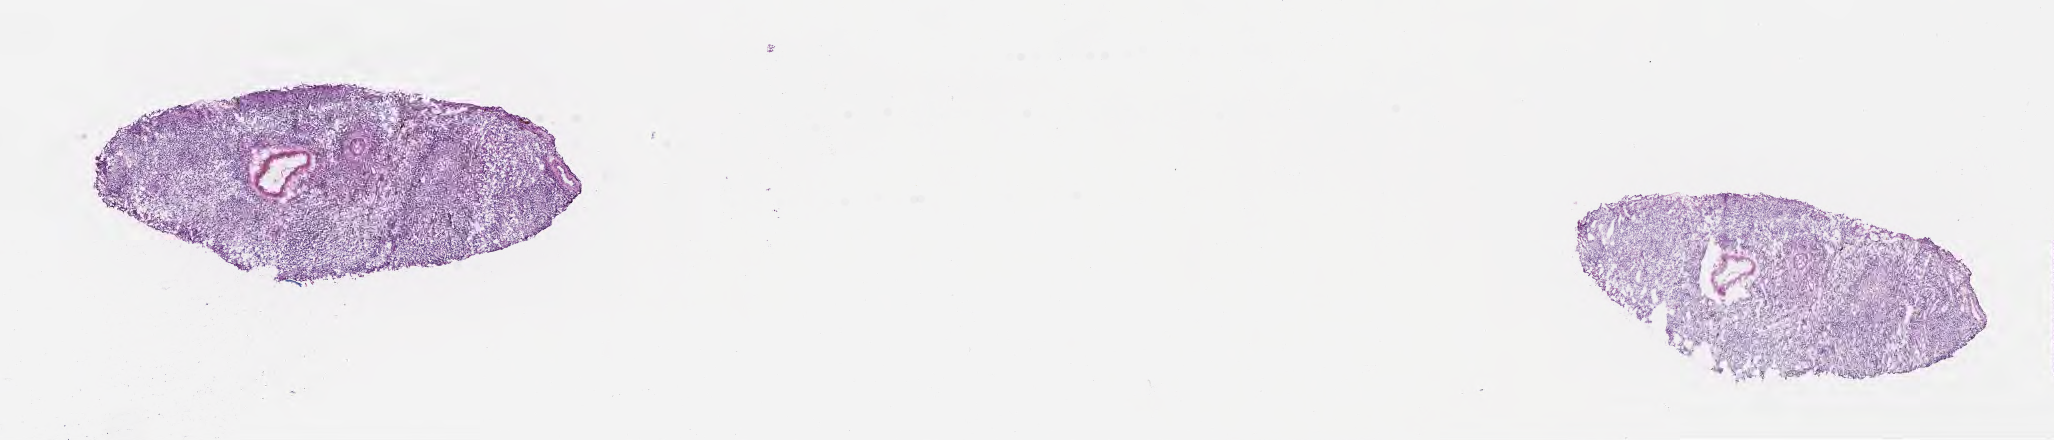
Digitized haematoxylin and eosin-stained section, whole scanned area (about 16.6 x 3.6 mm) shown as a low-resolution overview; frozen section (tissue freezing medium); primary tumor; anatomic site: brain. Patient: female, age at initial diagnosis 82 years. Composition of this section per pathologist review: tumor cells 92%, tumor nuclei 97%, stromal cells 2%, necrosis 3%, normal cells 3%. Inflammatory infiltration, as recorded: lymphocyte infiltration 0%, monocyte infiltration 0%, neutrophil infiltration 0%.
Section: top of the tissue portion. Histologic diagnosis: Glioblastoma, NOS.